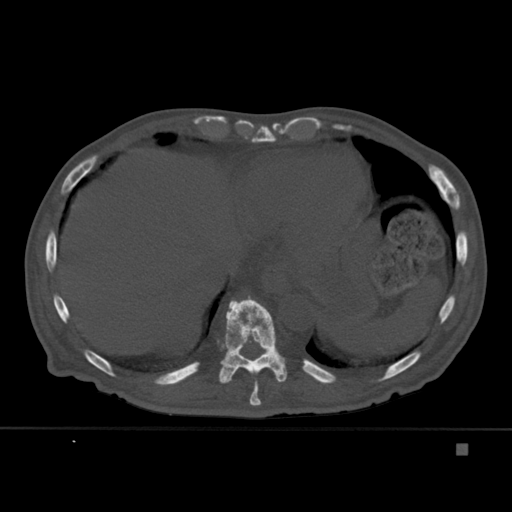
CT including the spine, one axial slice; slice 234 of 451 in the series (ordered by position); bone window (W 1800 / L 400 HU); 1.5 mm slice thickness; 512 × 512 image matrix, field of view 378 × 378 mm. Male patient, age 75 years. Case-level facts recorded for this patient, not image findings: primary cancer: prostate.
Outlined on this slice (semi-automatic segmentation, software-assisted and operator-edited):
- T10 vertebra: bounding box <219,295,288,383> (left, top, right, bottom; pixels)
- T9 vertebra: <249,380,261,406>